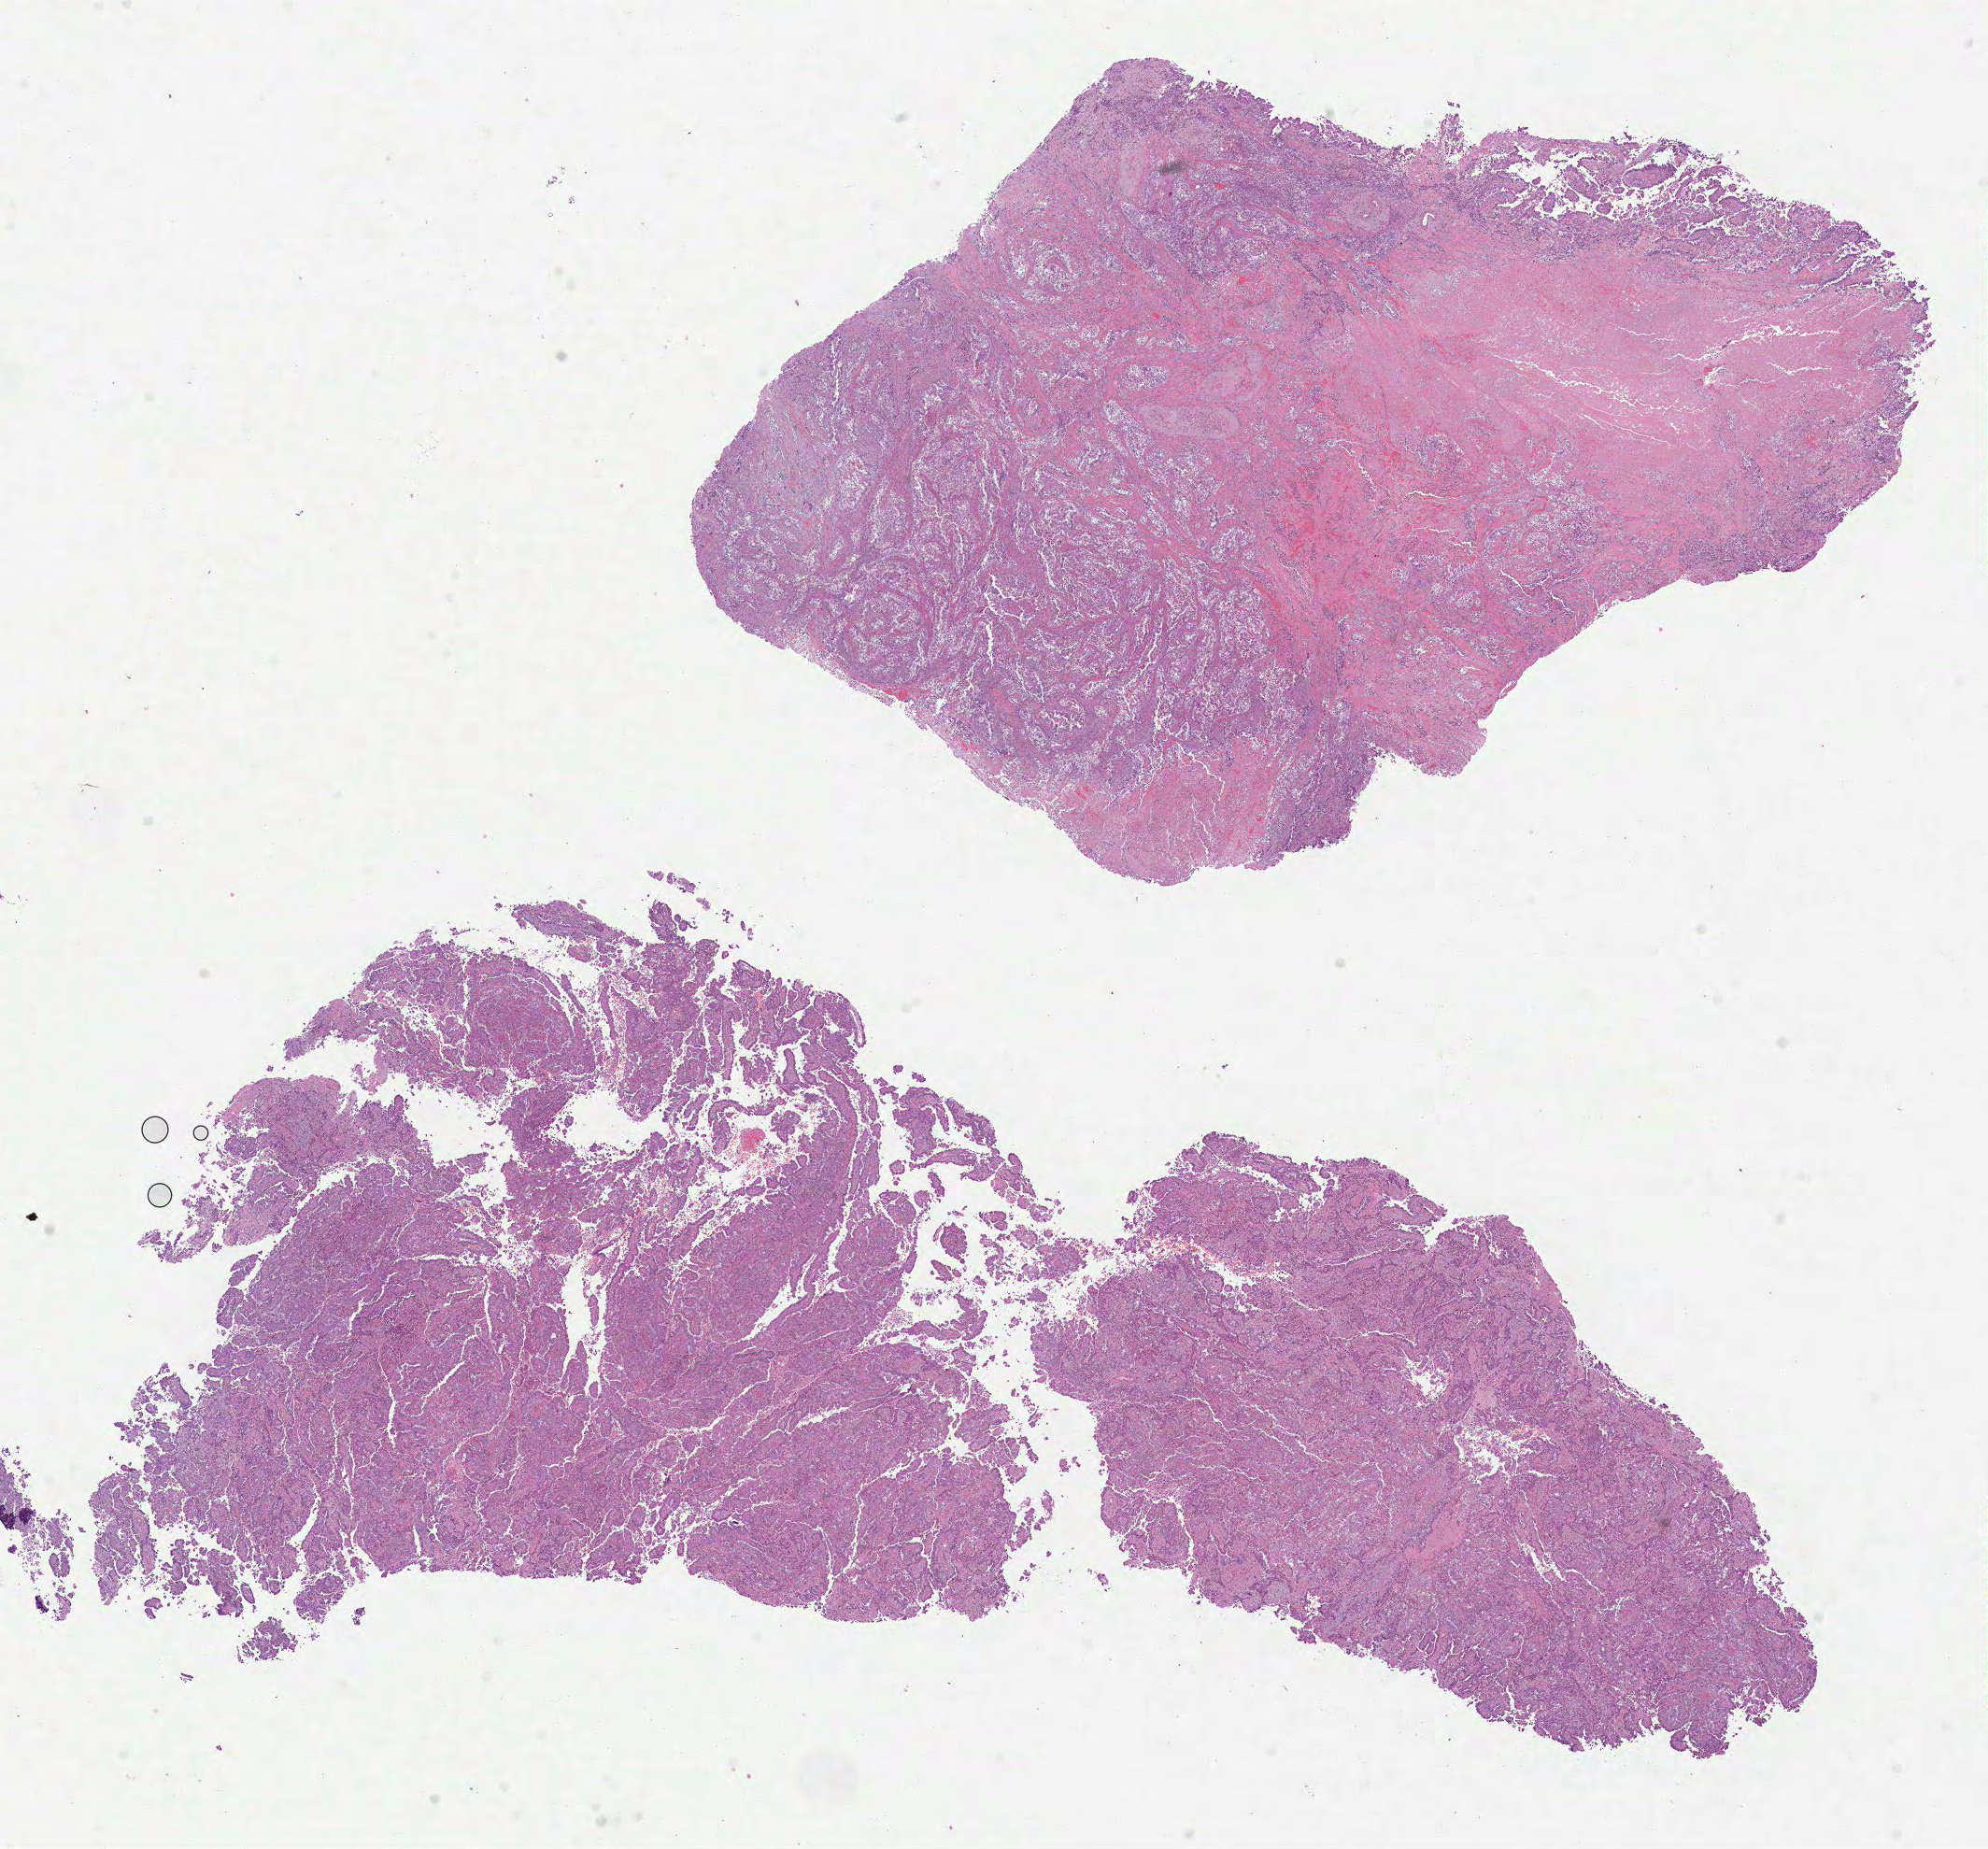
H&E whole-slide image — a low-resolution overview of the entire scanned area, about 17.2 x 16.0 mm (slide scanned at 40x); formalin-fixed paraffin-embedded (FFPE) diagnostic section; primary tumour sample from the uterus. Female, age 74 years at initial diagnosis. Histologic grade: G3 (poorly differentiated).
• lymph nodes positive (case pathology): 9 of 26 examined
• FIGO stage: IIIC2
• pathologic diagnosis: Serous cystadenocarcinoma, NOS (endometrium)